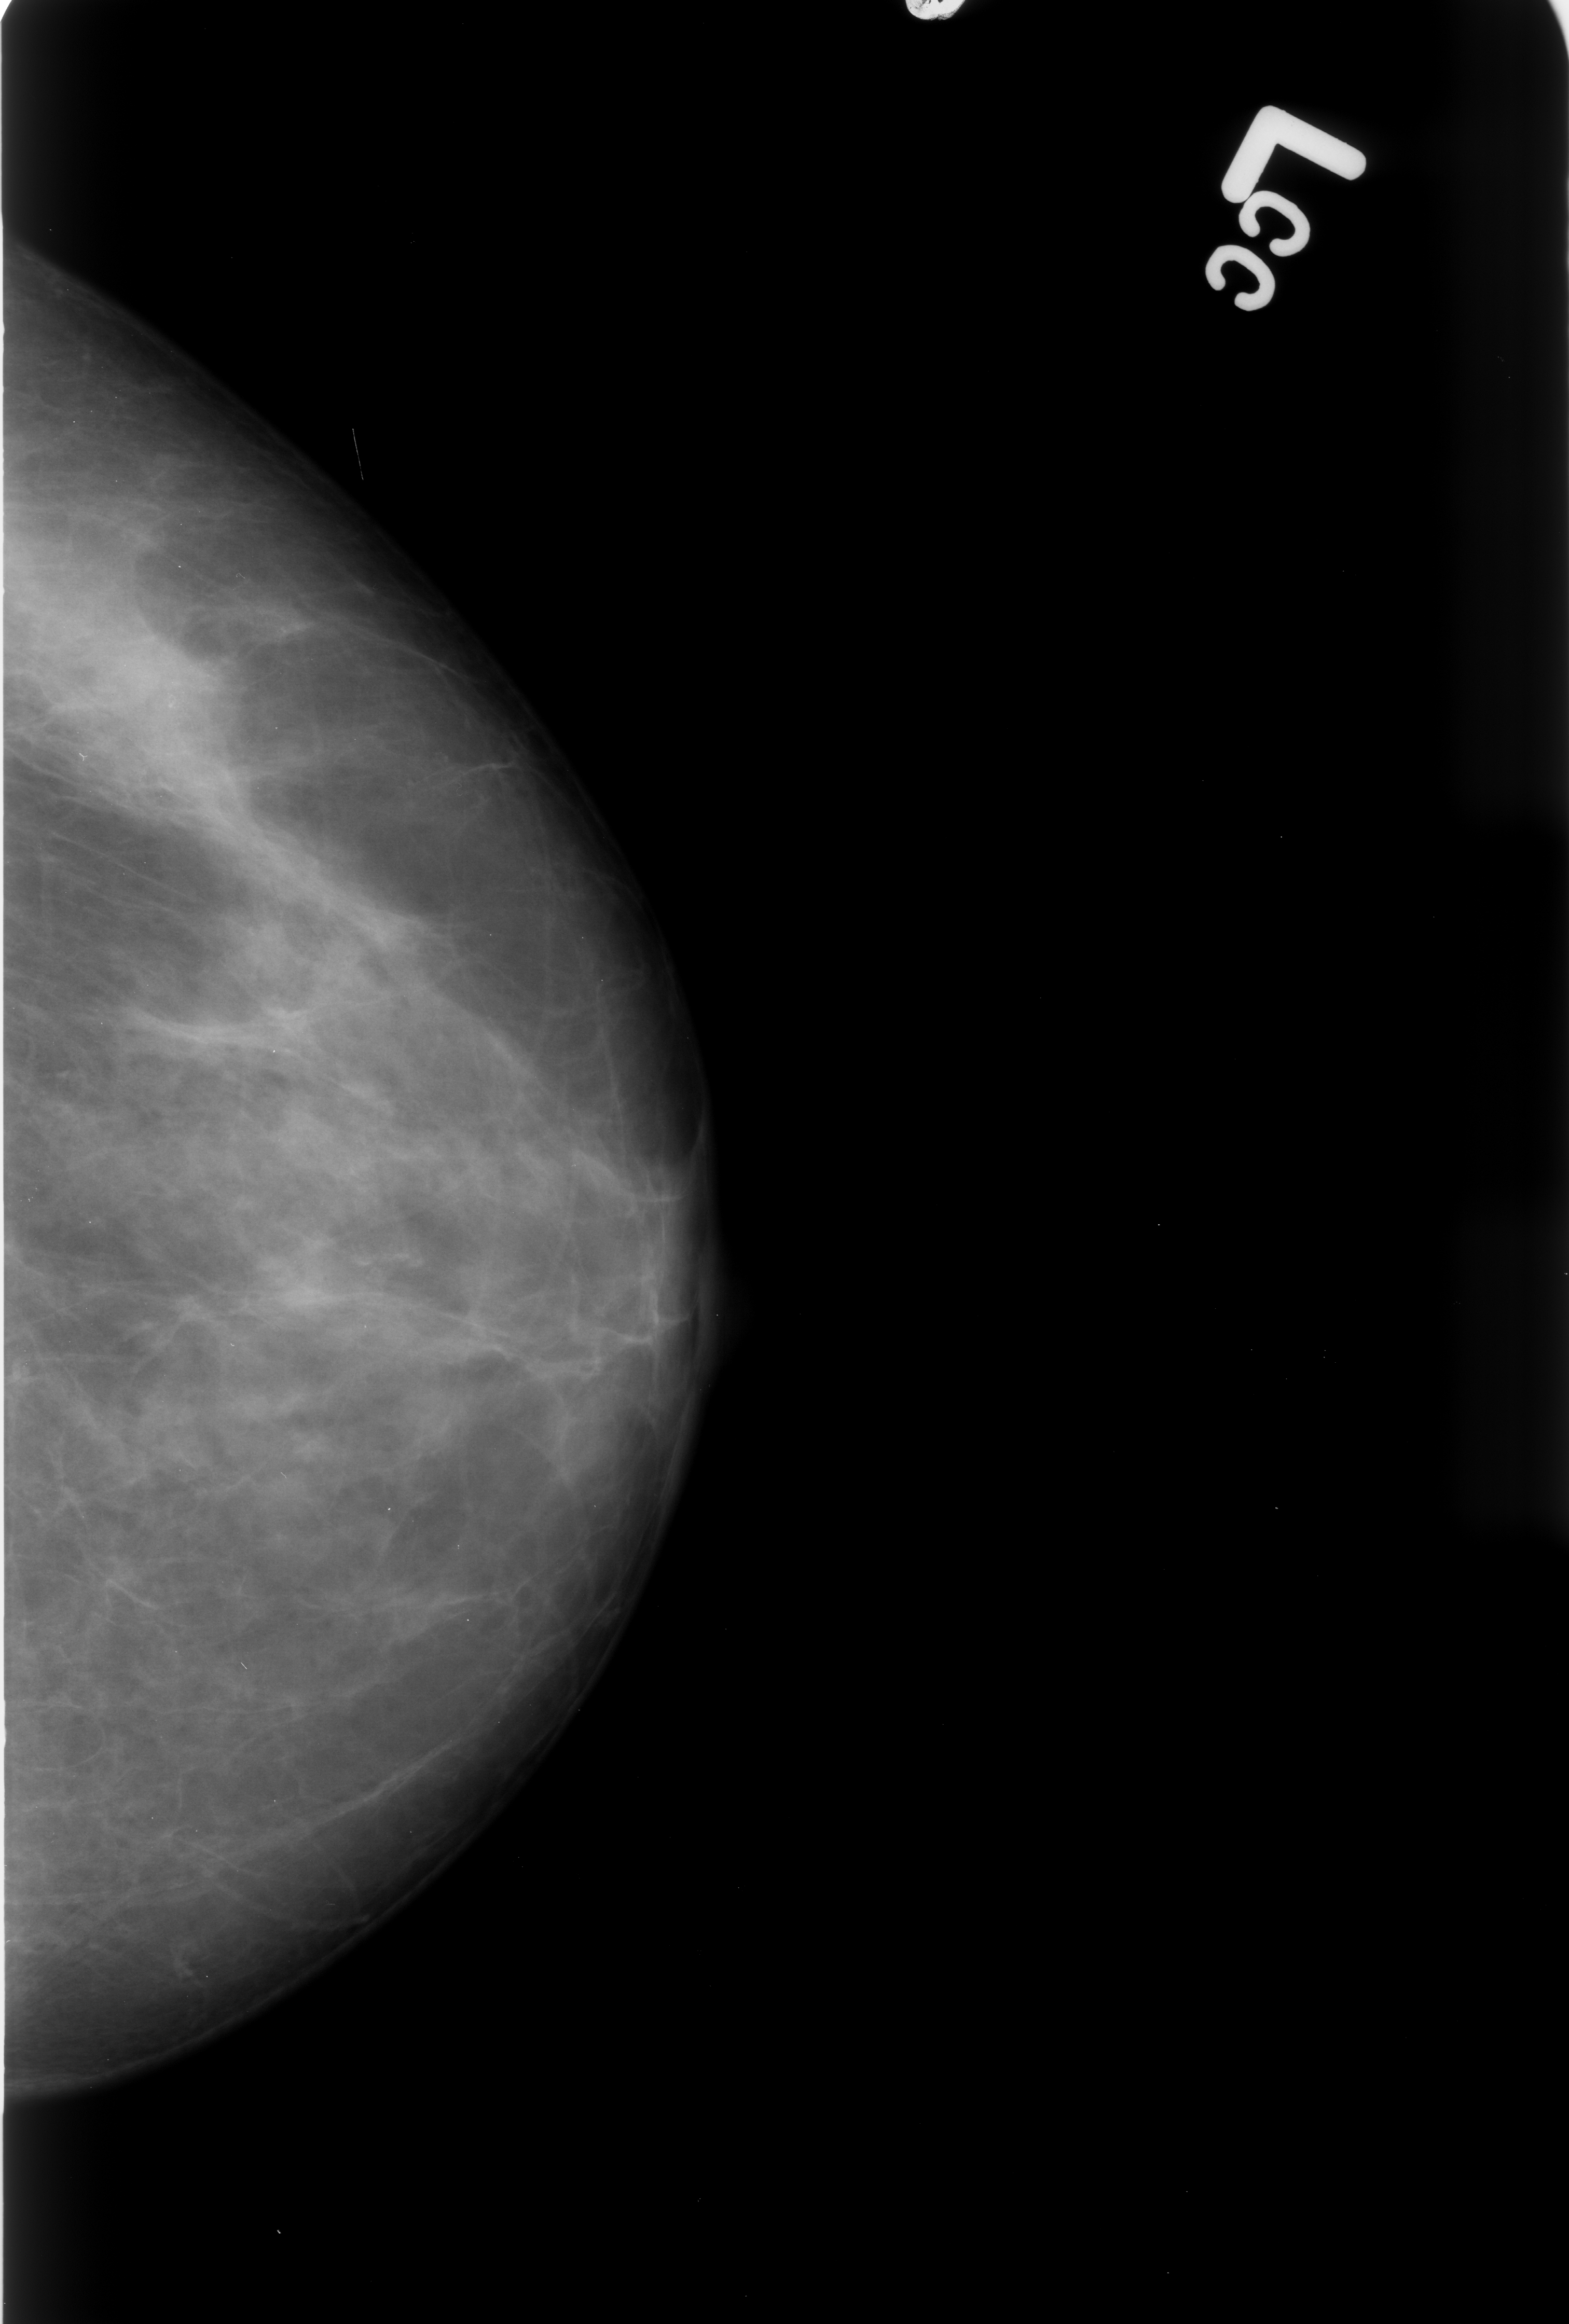
Digitized screen-film mammogram, left breast, CC view, breast composition: scattered fibroglandular densities (BI-RADS density category 2 of 4).
Abnormality record for this image: calcifications, morphology pleomorphic, distribution clustered; BI-RADS assessment category 4; pathology (as recorded): benign.